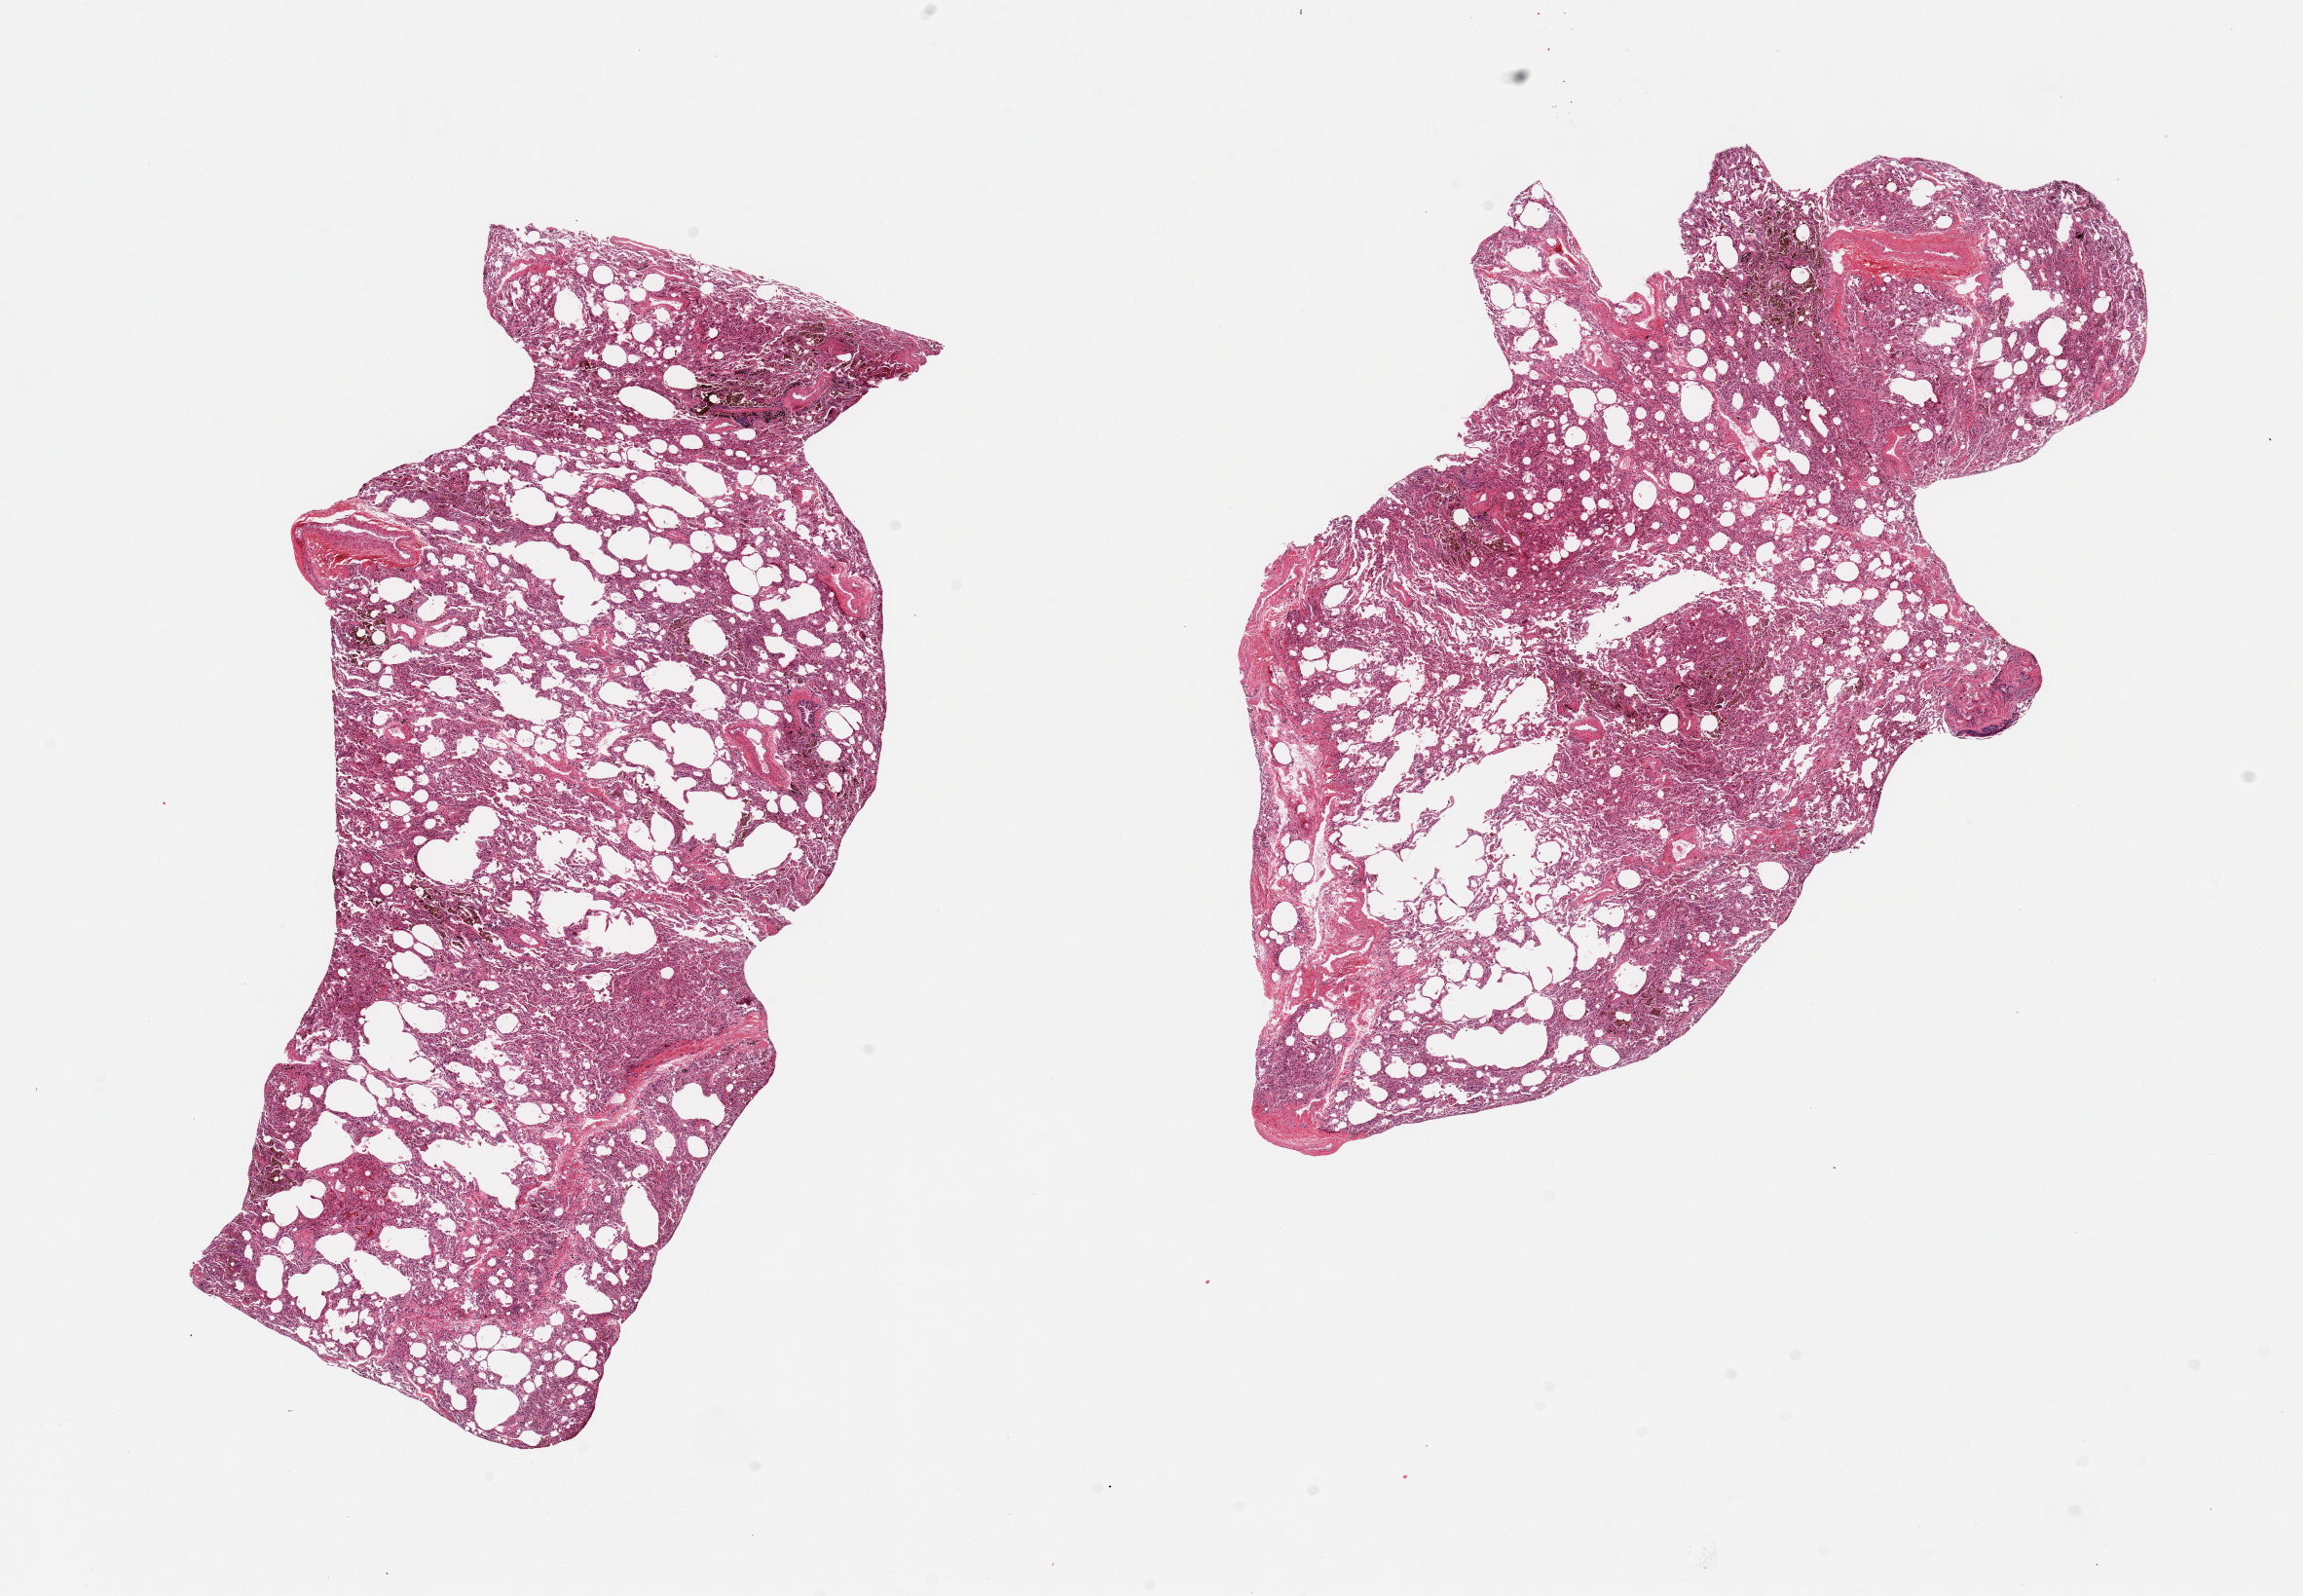
H&E whole-slide image, low-resolution overview of the scanned area, about 18.7 x 13.0 mm, PAXgene-fixed paraffin-embedded (PFPE) section, sampled site (target tissue): lung, tissue donor sample.
- review note (as recorded): 2 pieces; many pigmented macrophages present, some collapse, lymphocytic and focal acute inflammatory infiltrate